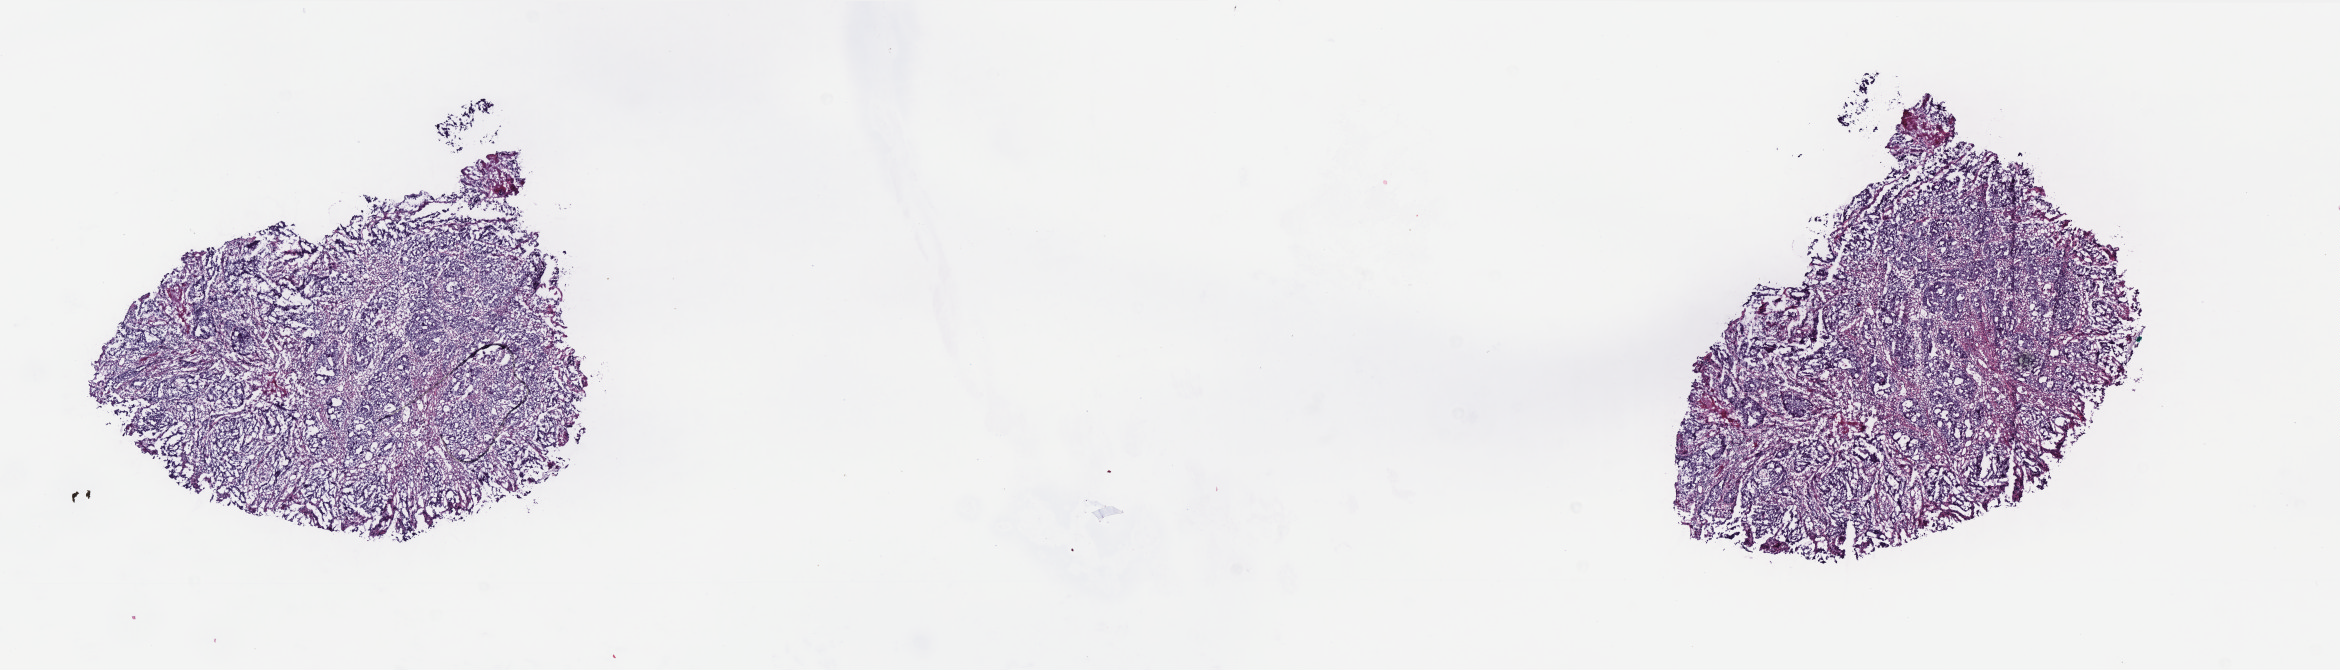
Digitized Hematoxylin and eosin (H&E) stained tissue section (whole slide), shown as a low-resolution overview of the whole scanned area (about 18.8 x 5.4 mm, acquisition: 40x scan), frozen section from the bottom of the tissue portion, primary tumour sample from the colon. Male, age 50 years at initial diagnosis. Composition of this section per pathologist review: tumour cells 96%, tumour nuclei 70%, normal cells 0%, stromal cells 0%, necrosis 4%. Infiltration values recorded for this section: lymphocyte infiltration 8%, monocyte infiltration 5%, neutrophil infiltration 5%.
• AJCC pathologic stage: IIIB (6th edition)
• histologic diagnosis: Adenocarcinoma, NOS (ascending colon)